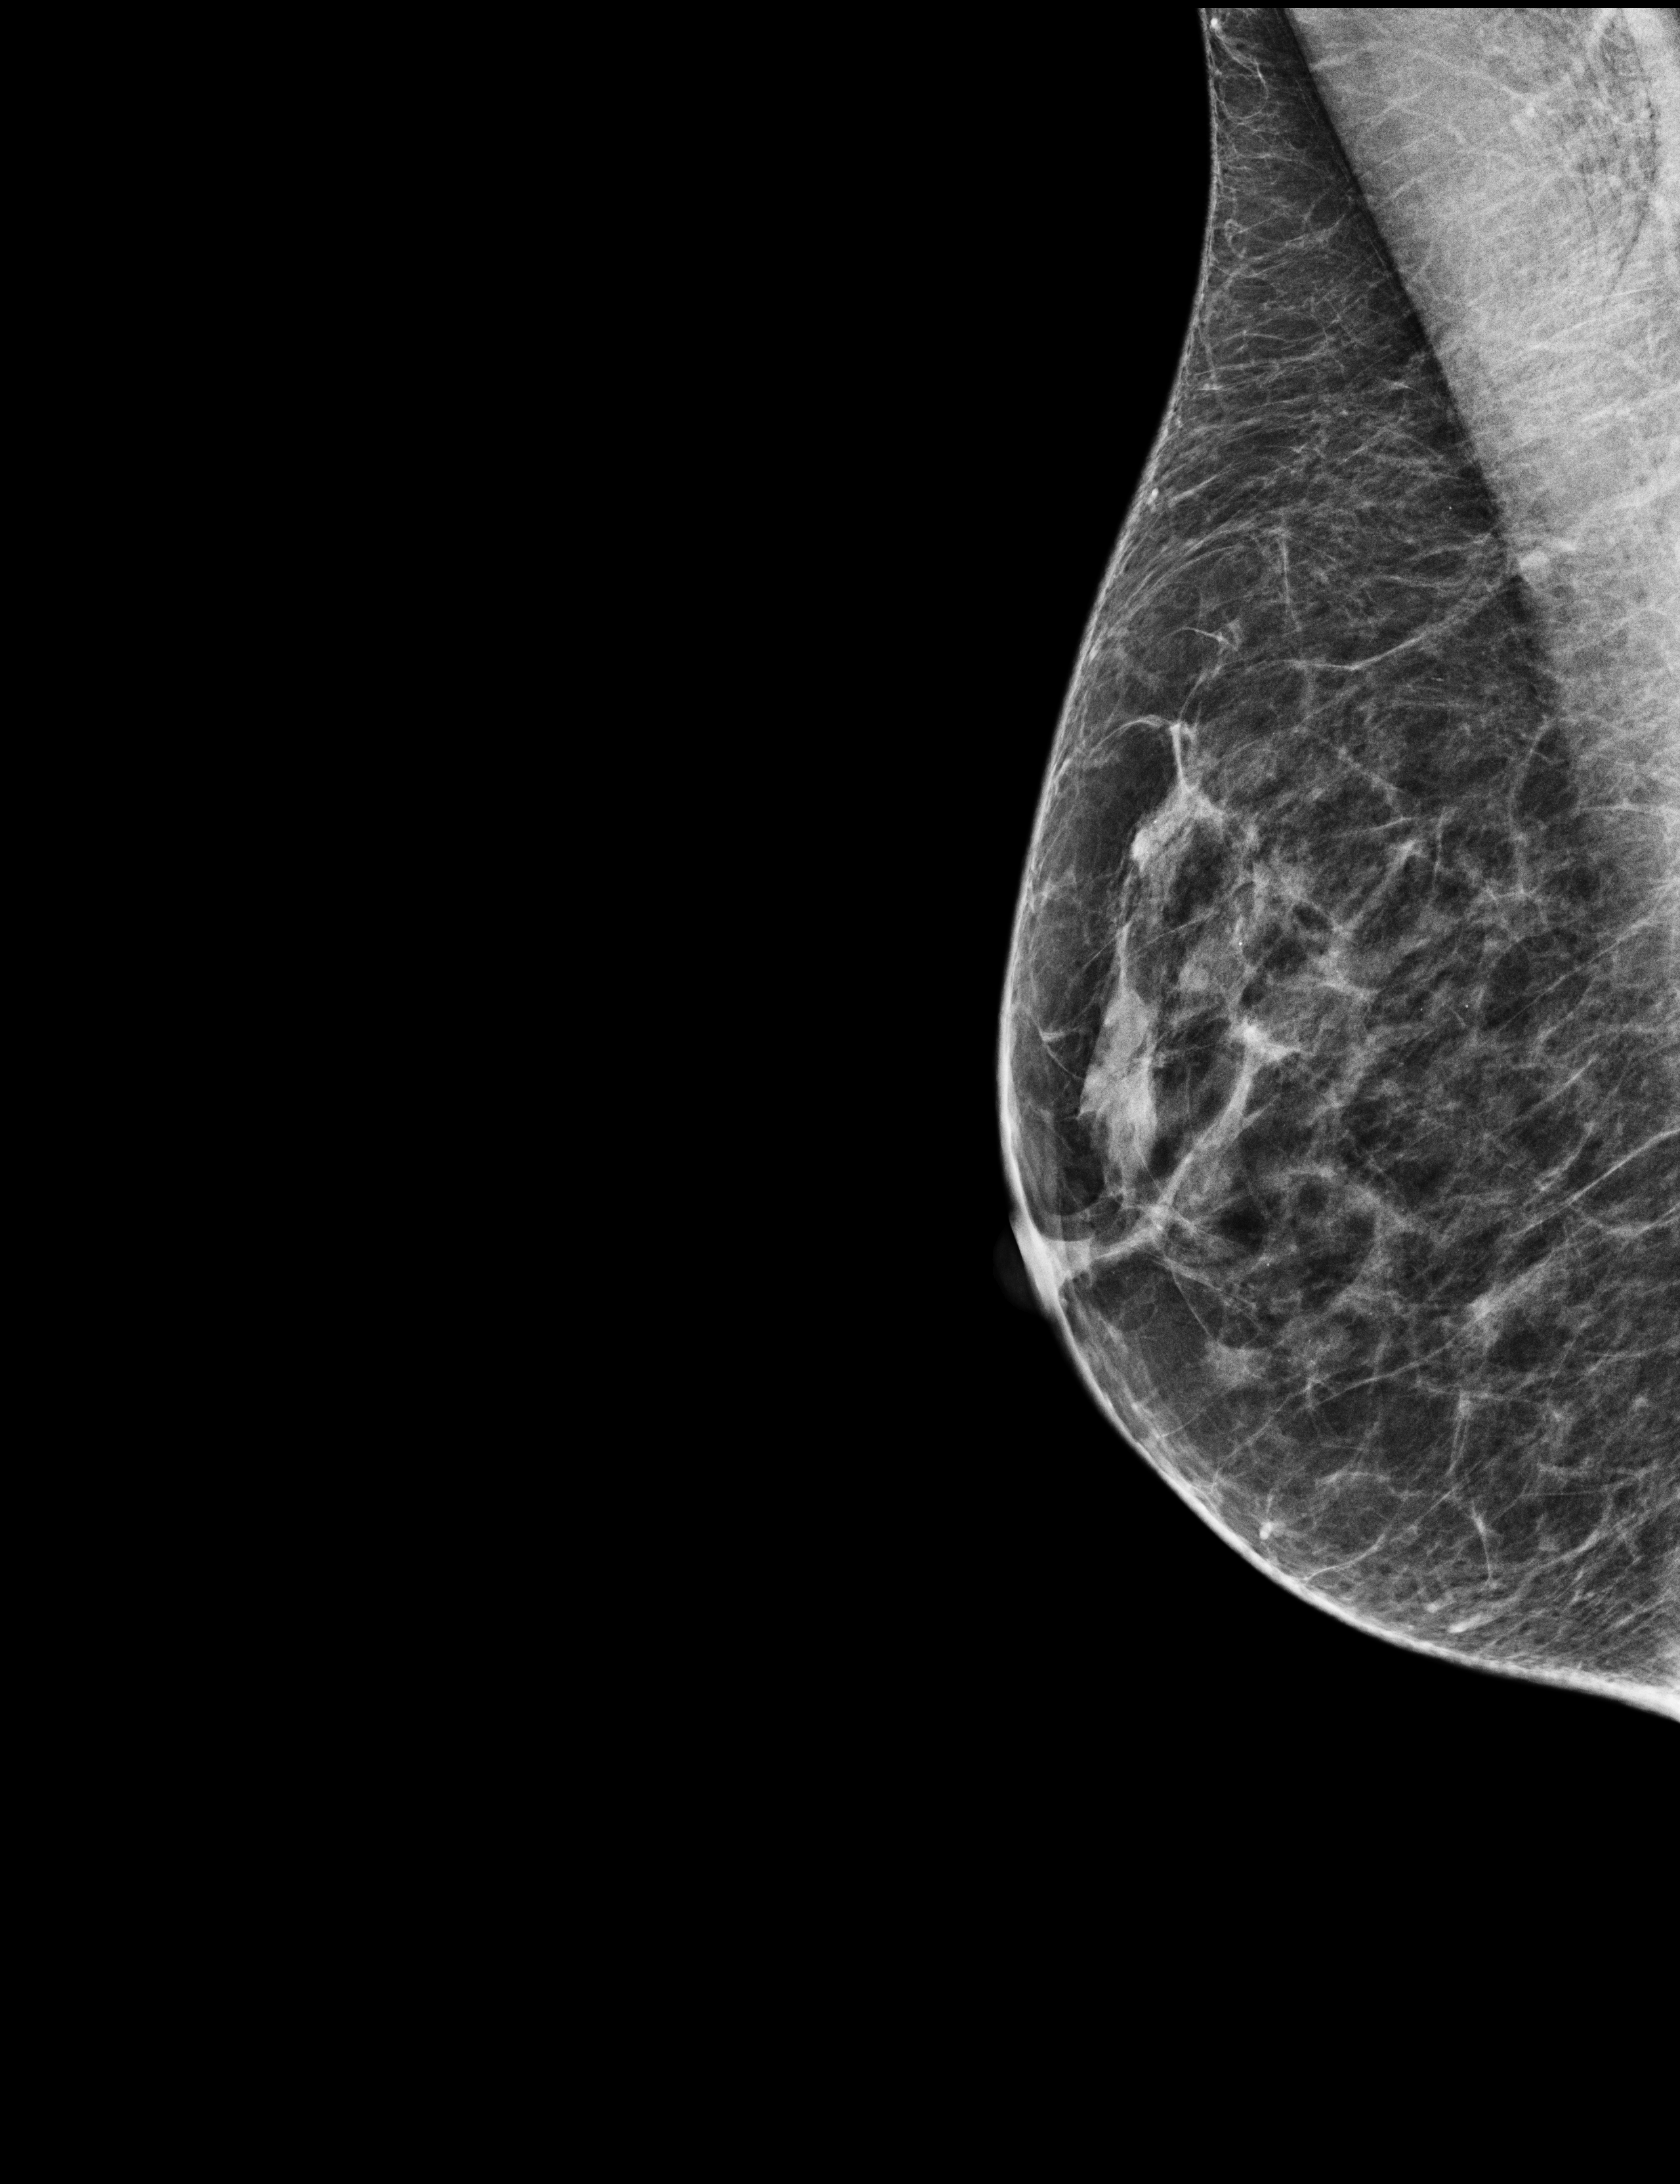
Annual screening mammography examination; compressed breast thickness 33 mm; system: Selenia Dimensions. Patient aged 68 years (female).
Image type: full-field digital mammogram. Breast: right. Projection: medio-lateral oblique projection.